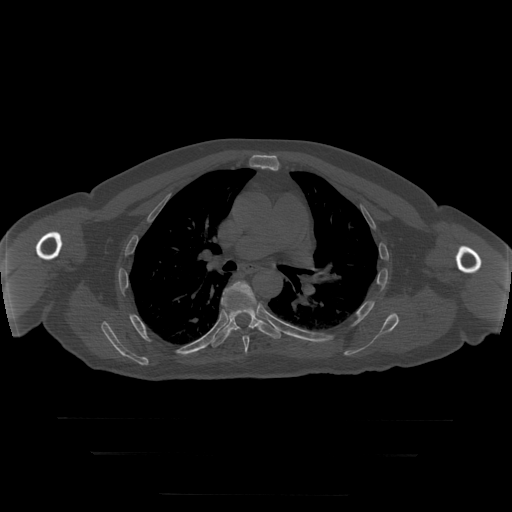
CT including the spine, one axial slice; slice 196 of 397 in the series (ordered by position); 120 kVp; bone window (W 1800 / L 400 HU); 512 × 512 image matrix. Patient age 73 years. Case-level facts recorded for this patient, not image findings: primary cancer: prostate.
Outlined on this slice (semi-automatically segmented with operator editing):
- T6 vertebra: bounding box (x1, y1, x2, y2) in pixels: (222, 282, 257, 355)
- T7 vertebra: (210, 308, 281, 348)